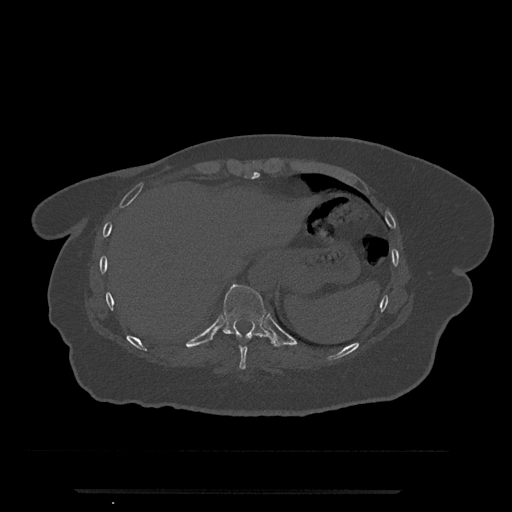
CT including the spine, one axial slice; position 305 of 797 along the scan axis; reconstruction kernel Br40s/3; 120 kVp; bone window (W 1800 / L 400 HU); 512 × 512 image matrix, field of view 440 × 440 mm. Female patient, age 51 years. Case-level facts recorded for this patient, not image findings: primary cancer: neuro; vertebrae with lytic lesions (as recorded): T8.
Outlined on this slice (semi-automatically segmented with operator editing):
- T10 vertebra: bounding box [x1, y1, x2, y2] px = [222, 284, 277, 347]
- T9 vertebra: [239, 345, 247, 370]